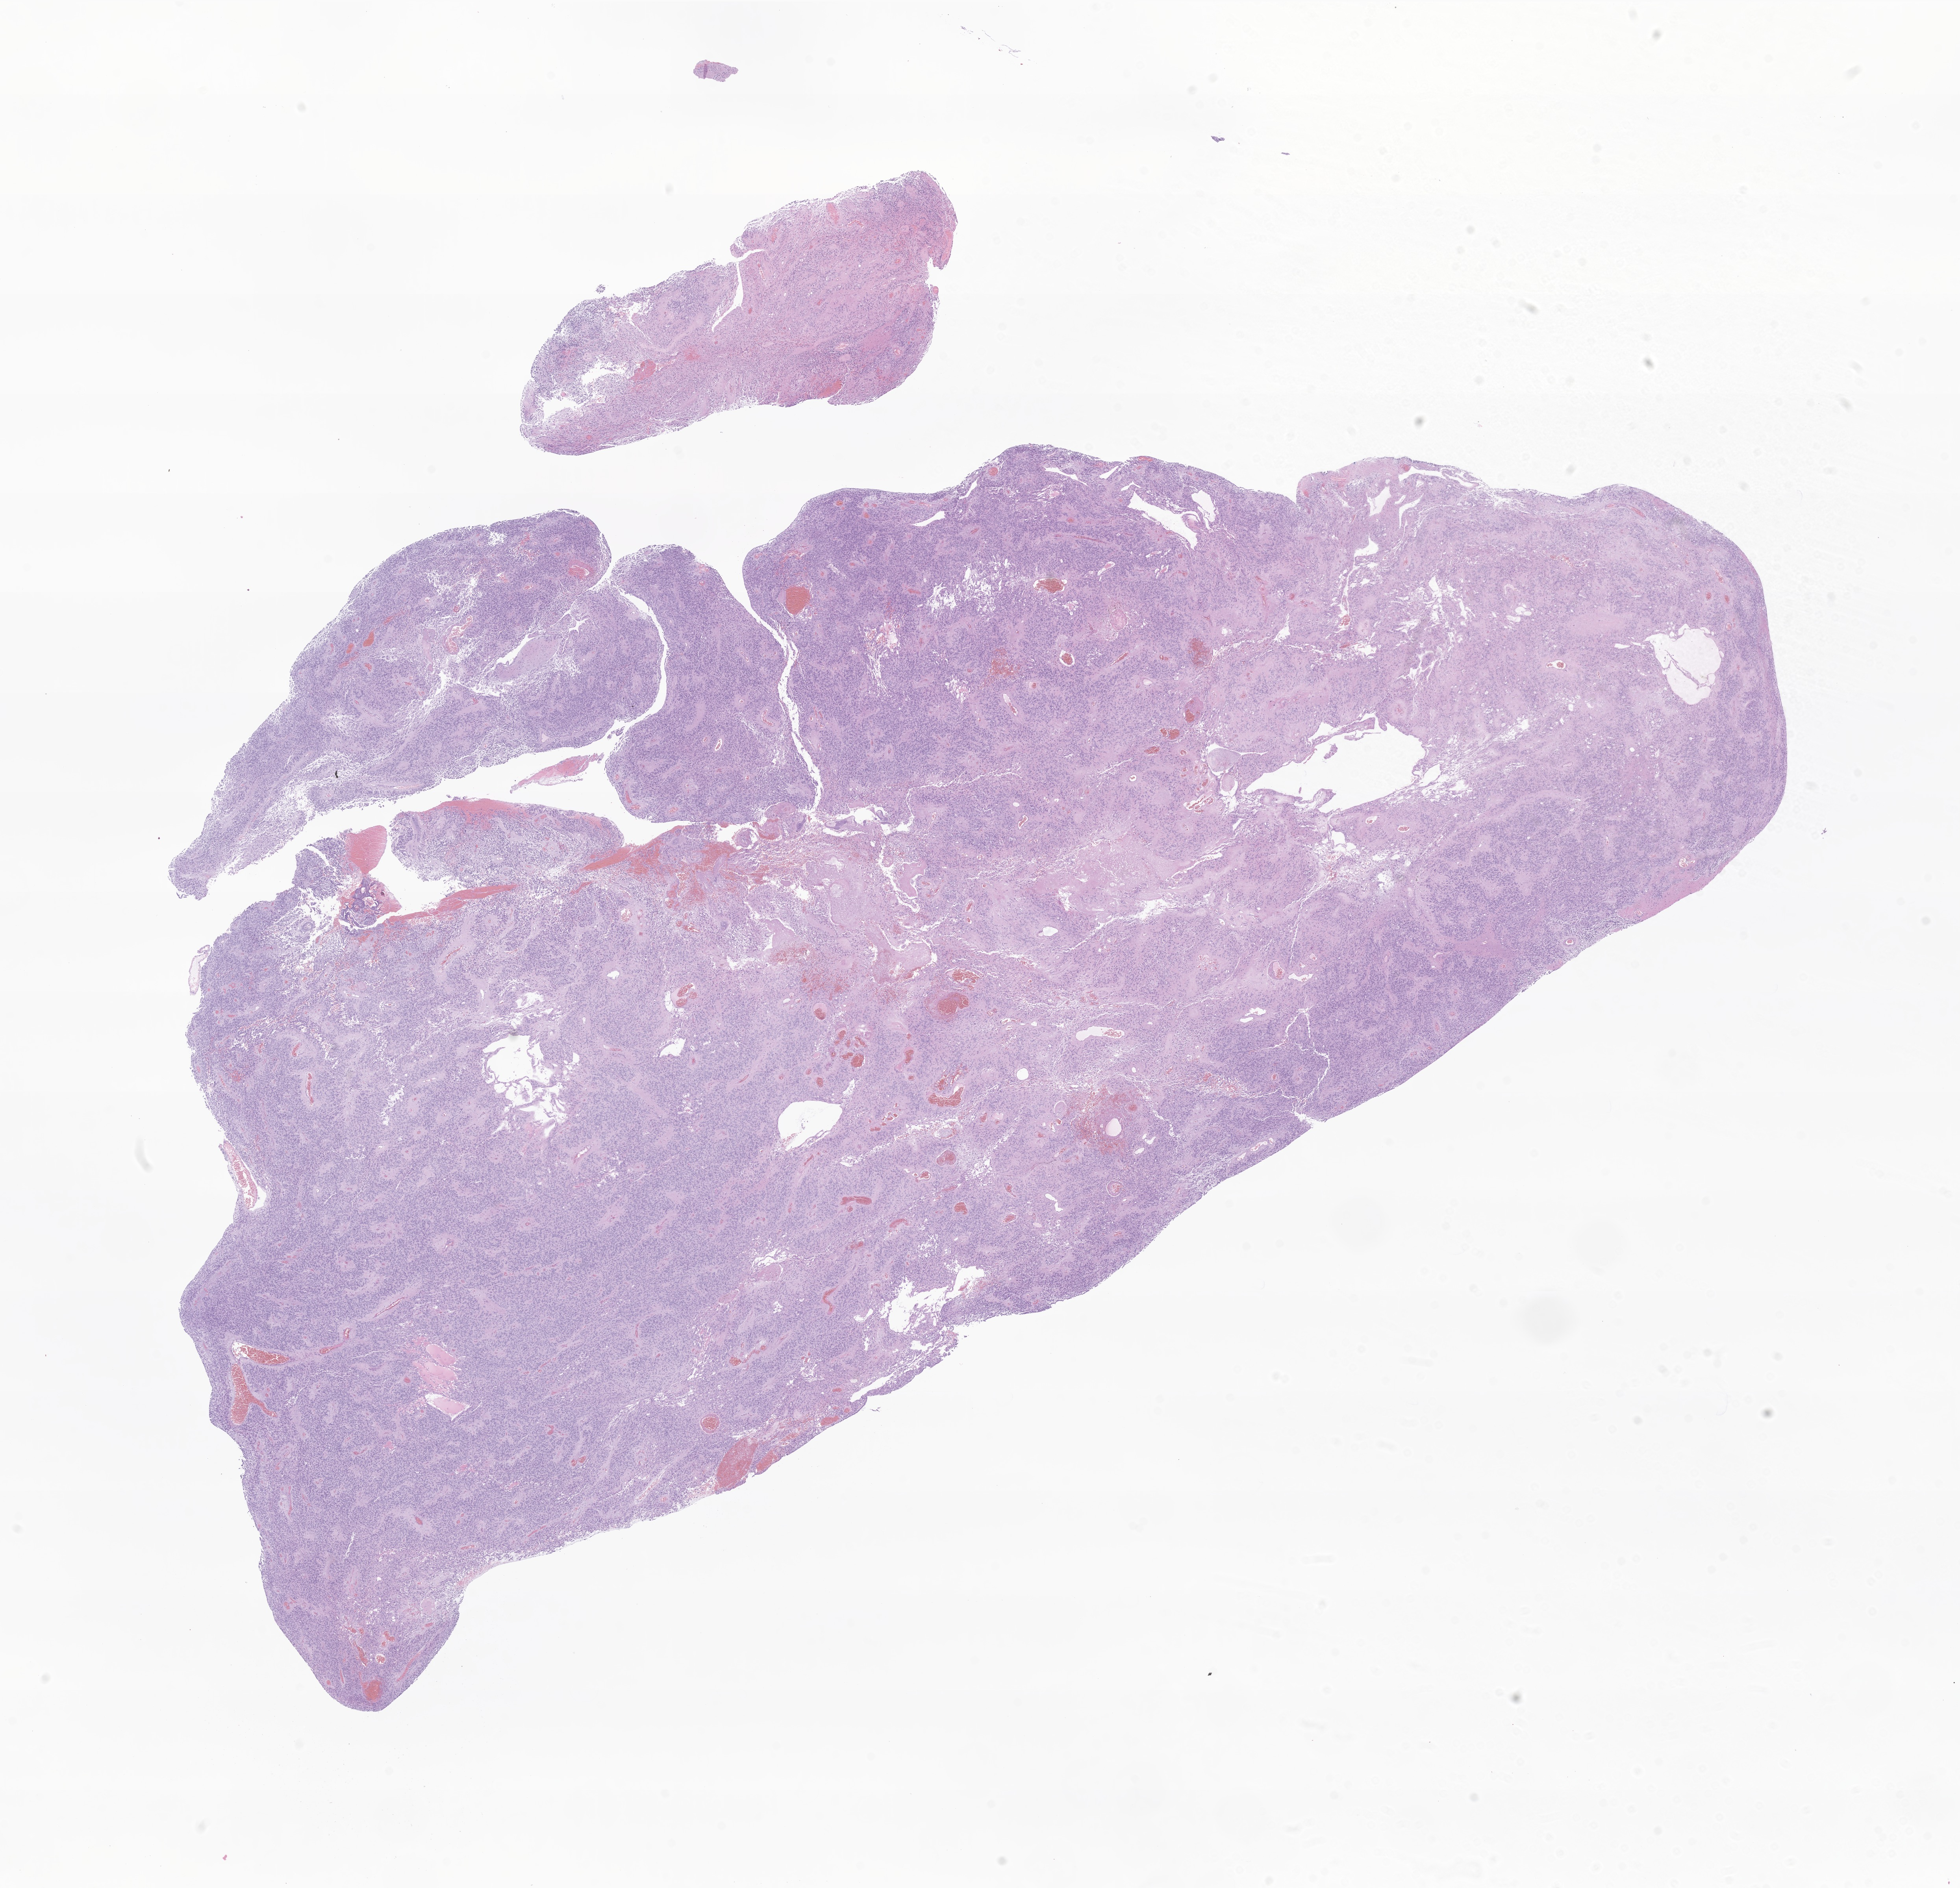
H&E whole-slide image of tumor tissue from the brain — whole scanned area (about 21.0 x 20.2 mm) shown as a low-resolution overview, formalin-fixed paraffin-embedded section. Patient: male, age 166 months (13 years 10 months).
Recorded diagnosis: Ependymoma, NOS.